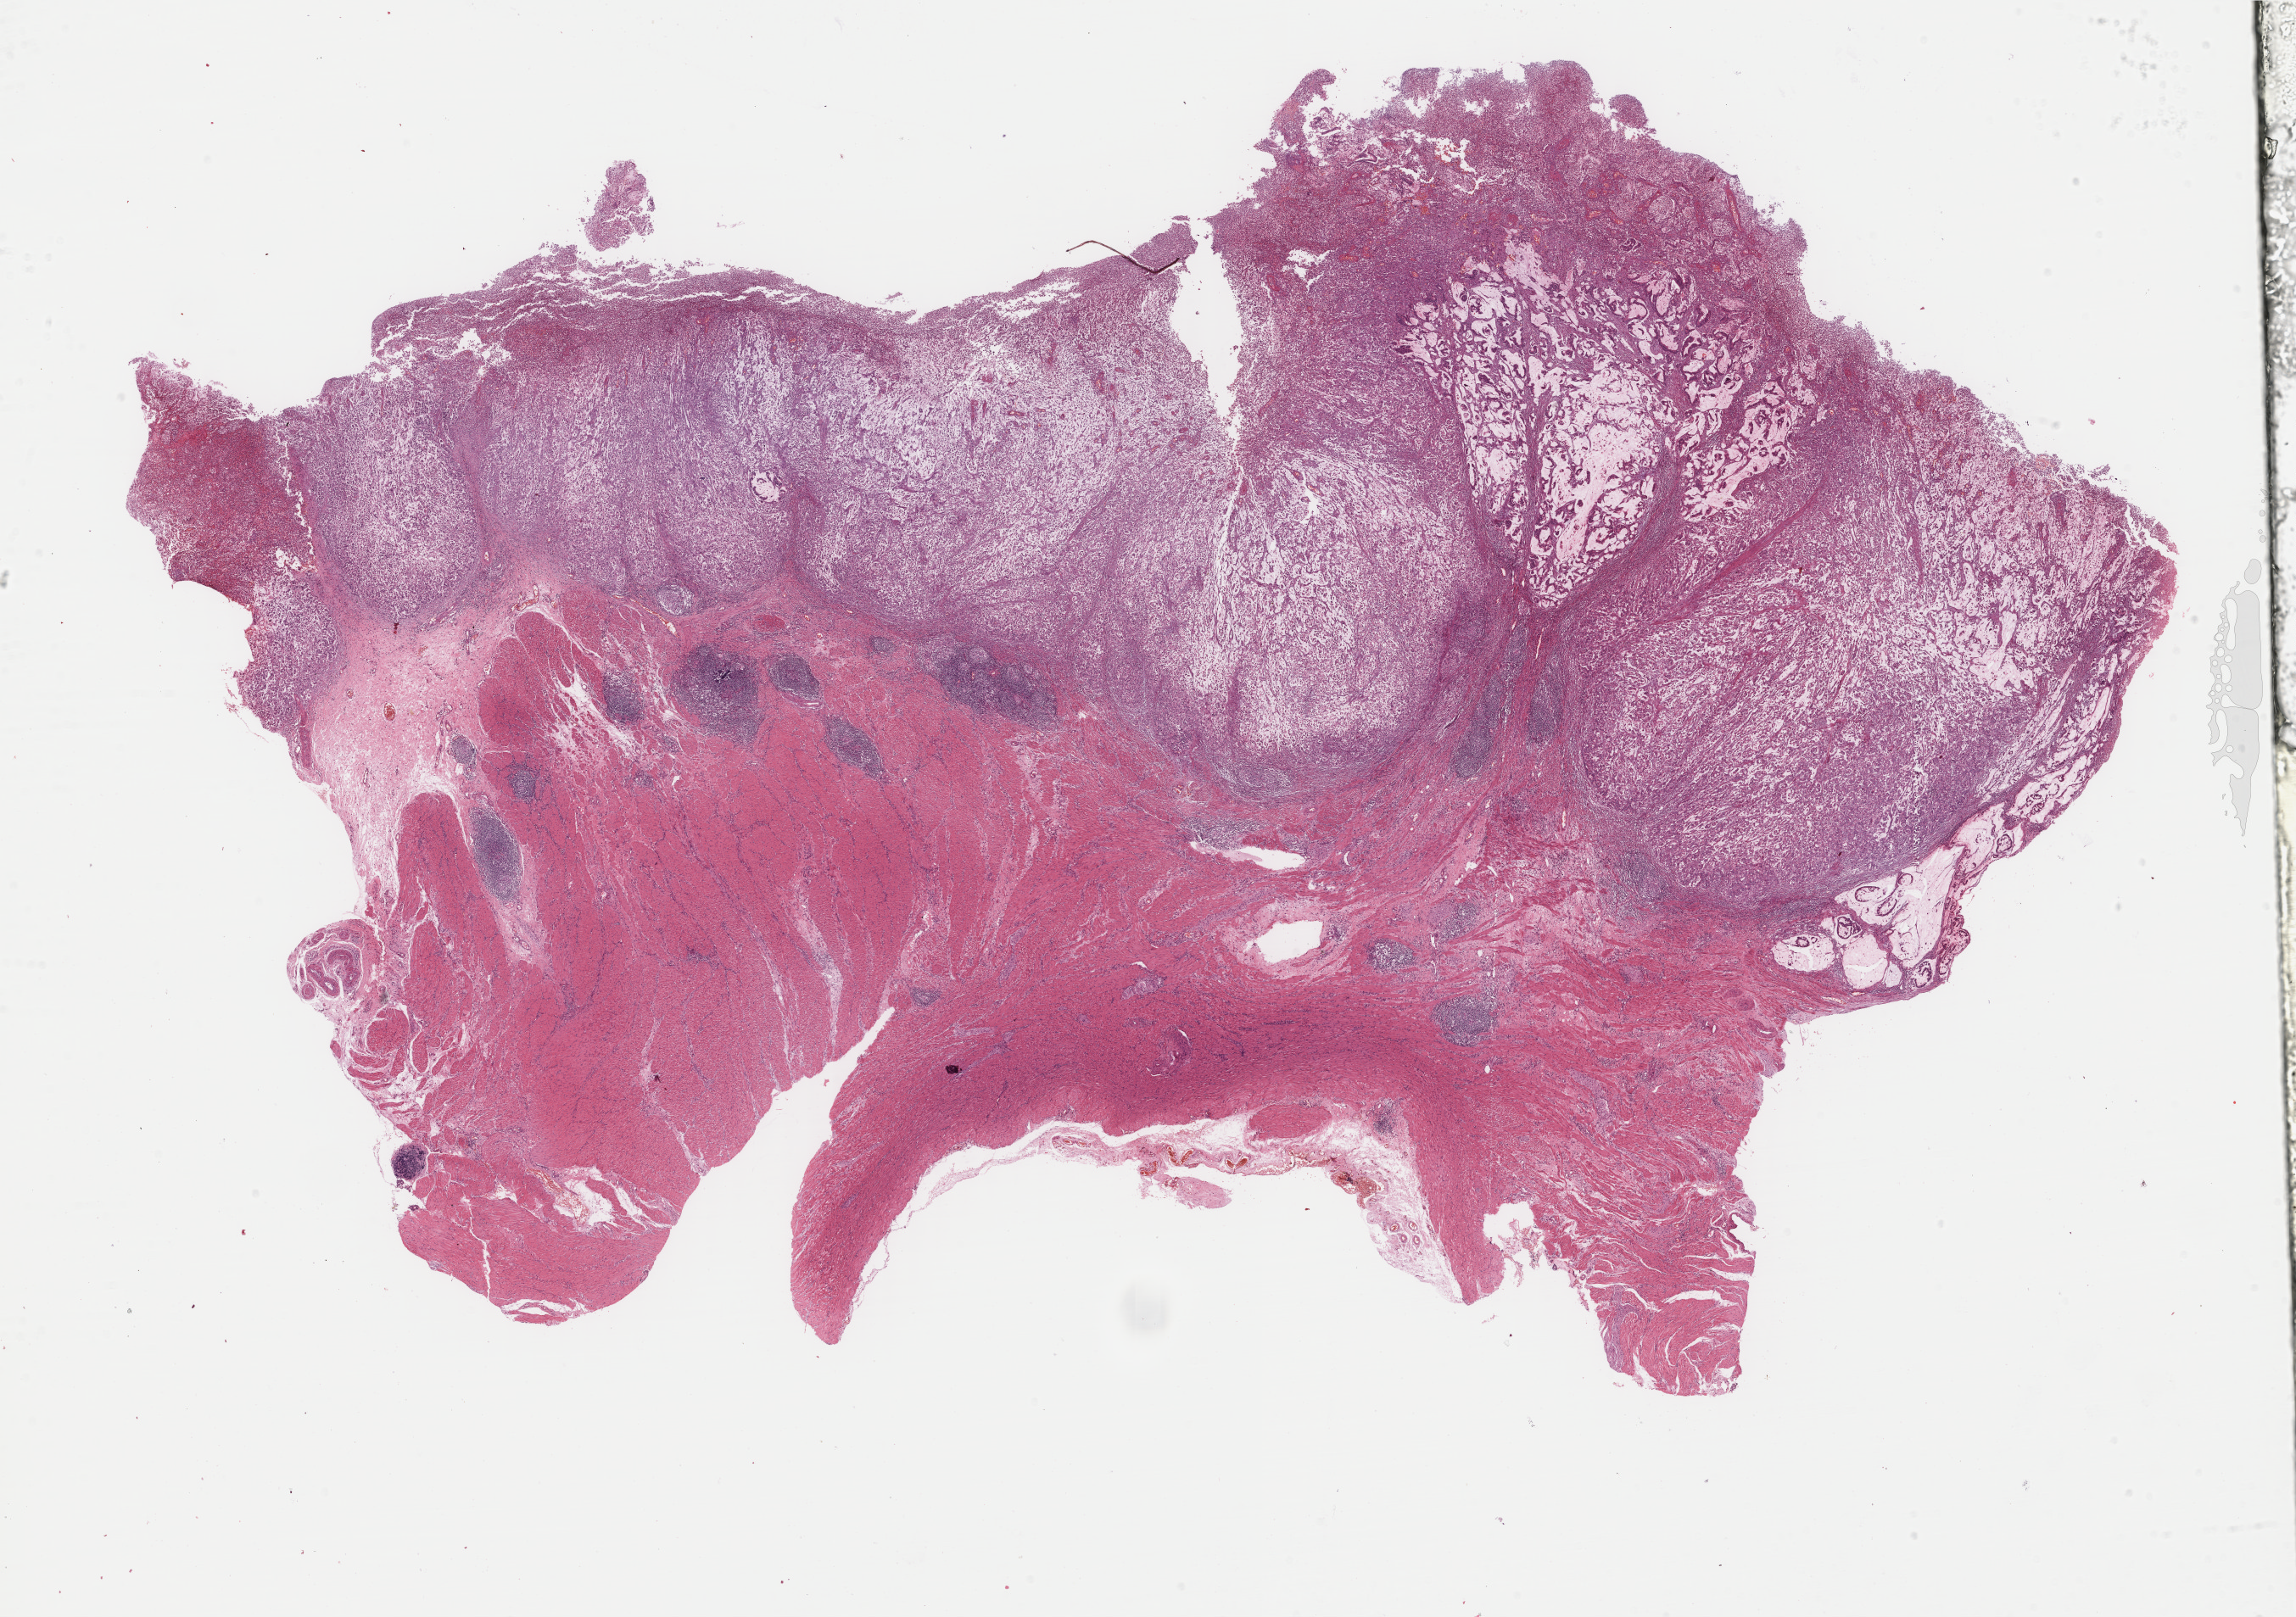
Digitized H&E tissue section (whole slide), whole scanned area (about 21.5 x 15.1 mm) shown as a low-resolution overview. Formalin-fixed paraffin-embedded (FFPE) diagnostic section. Primary tumour sample from the stomach. Patient: male, age at initial diagnosis 76 years. Histologic grade: G3 (poorly differentiated).
AJCC pathologic stage: IIA (7th edition). Pathologic diagnosis: Carcinoma, diffuse type (cardia, NOS).